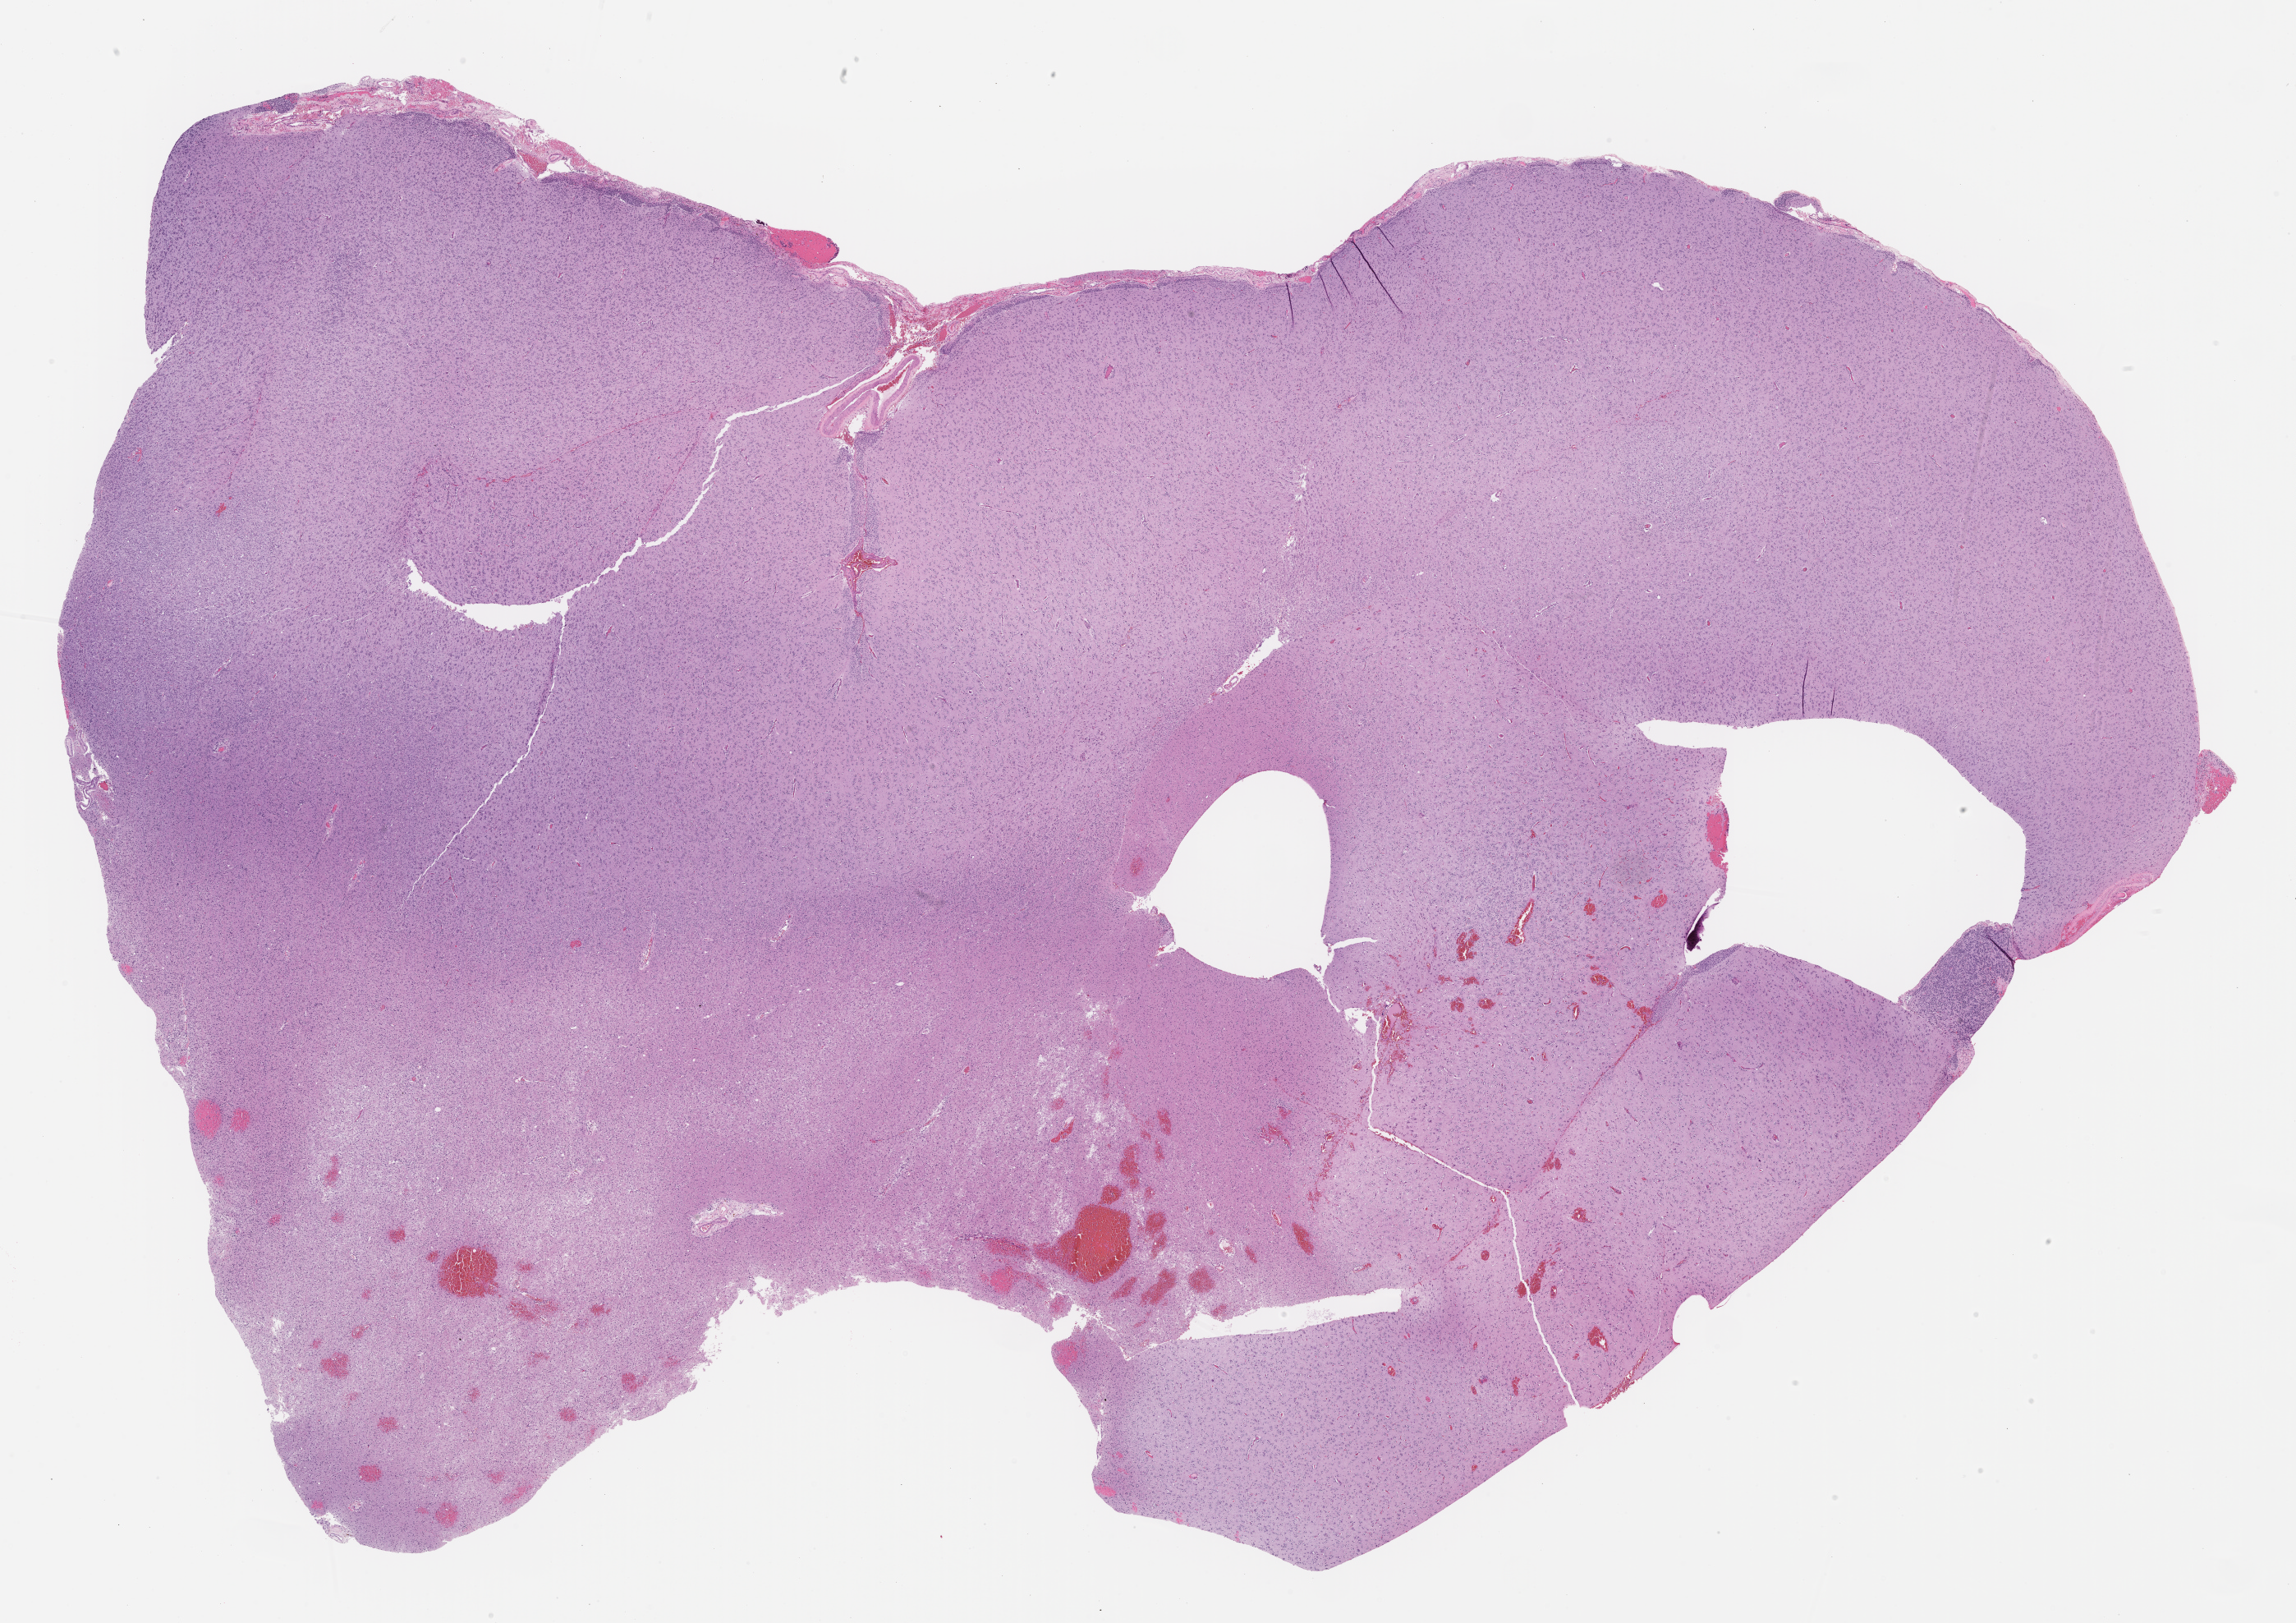
Digitized Hematoxylin and eosin (H&E) stained tissue section (whole slide) — whole scanned area (about 22.5 x 15.9 mm) shown as a low-resolution overview. Formalin-fixed paraffin-embedded (FFPE) diagnostic section. Primary tumour sample from the brain. Female, age 53 years at initial diagnosis. Histologic grade: G2 (moderately differentiated).
Laterality: right. Pathologic diagnosis: Oligodendroglioma, NOS (cerebrum).